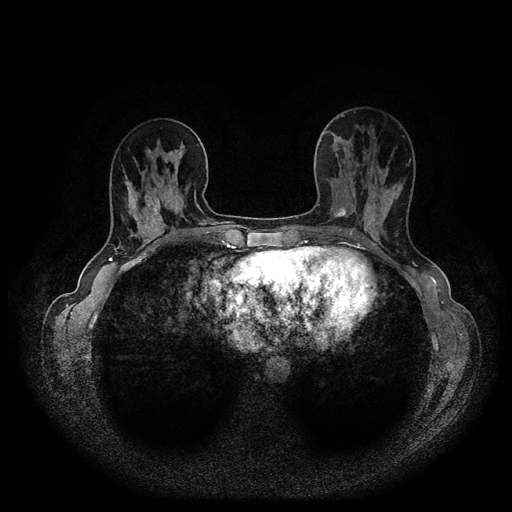
Breast MRI (dynamic contrast-enhanced, multi-phase), one axial slice; slice 37 of 116 in the series (ordered by position); dynamic contrast-enhanced series, time point 2 of 5 at this slice position (early post-contrast); 1.5 T; TE 2.6 ms, TR 5.4 ms; 2 mm slice thickness; 512 × 512 image matrix, field of view 340 × 340 mm. Patient: female, 40 years.
Annotated regions visible in this slice (semi-automatically segmented with operator editing):
- breast lesion (labelled 'tumour' in the annotation; benign lesions carry a separate 'benign' label): bounding box <334,206,347,218> (left, top, right, bottom; pixels)